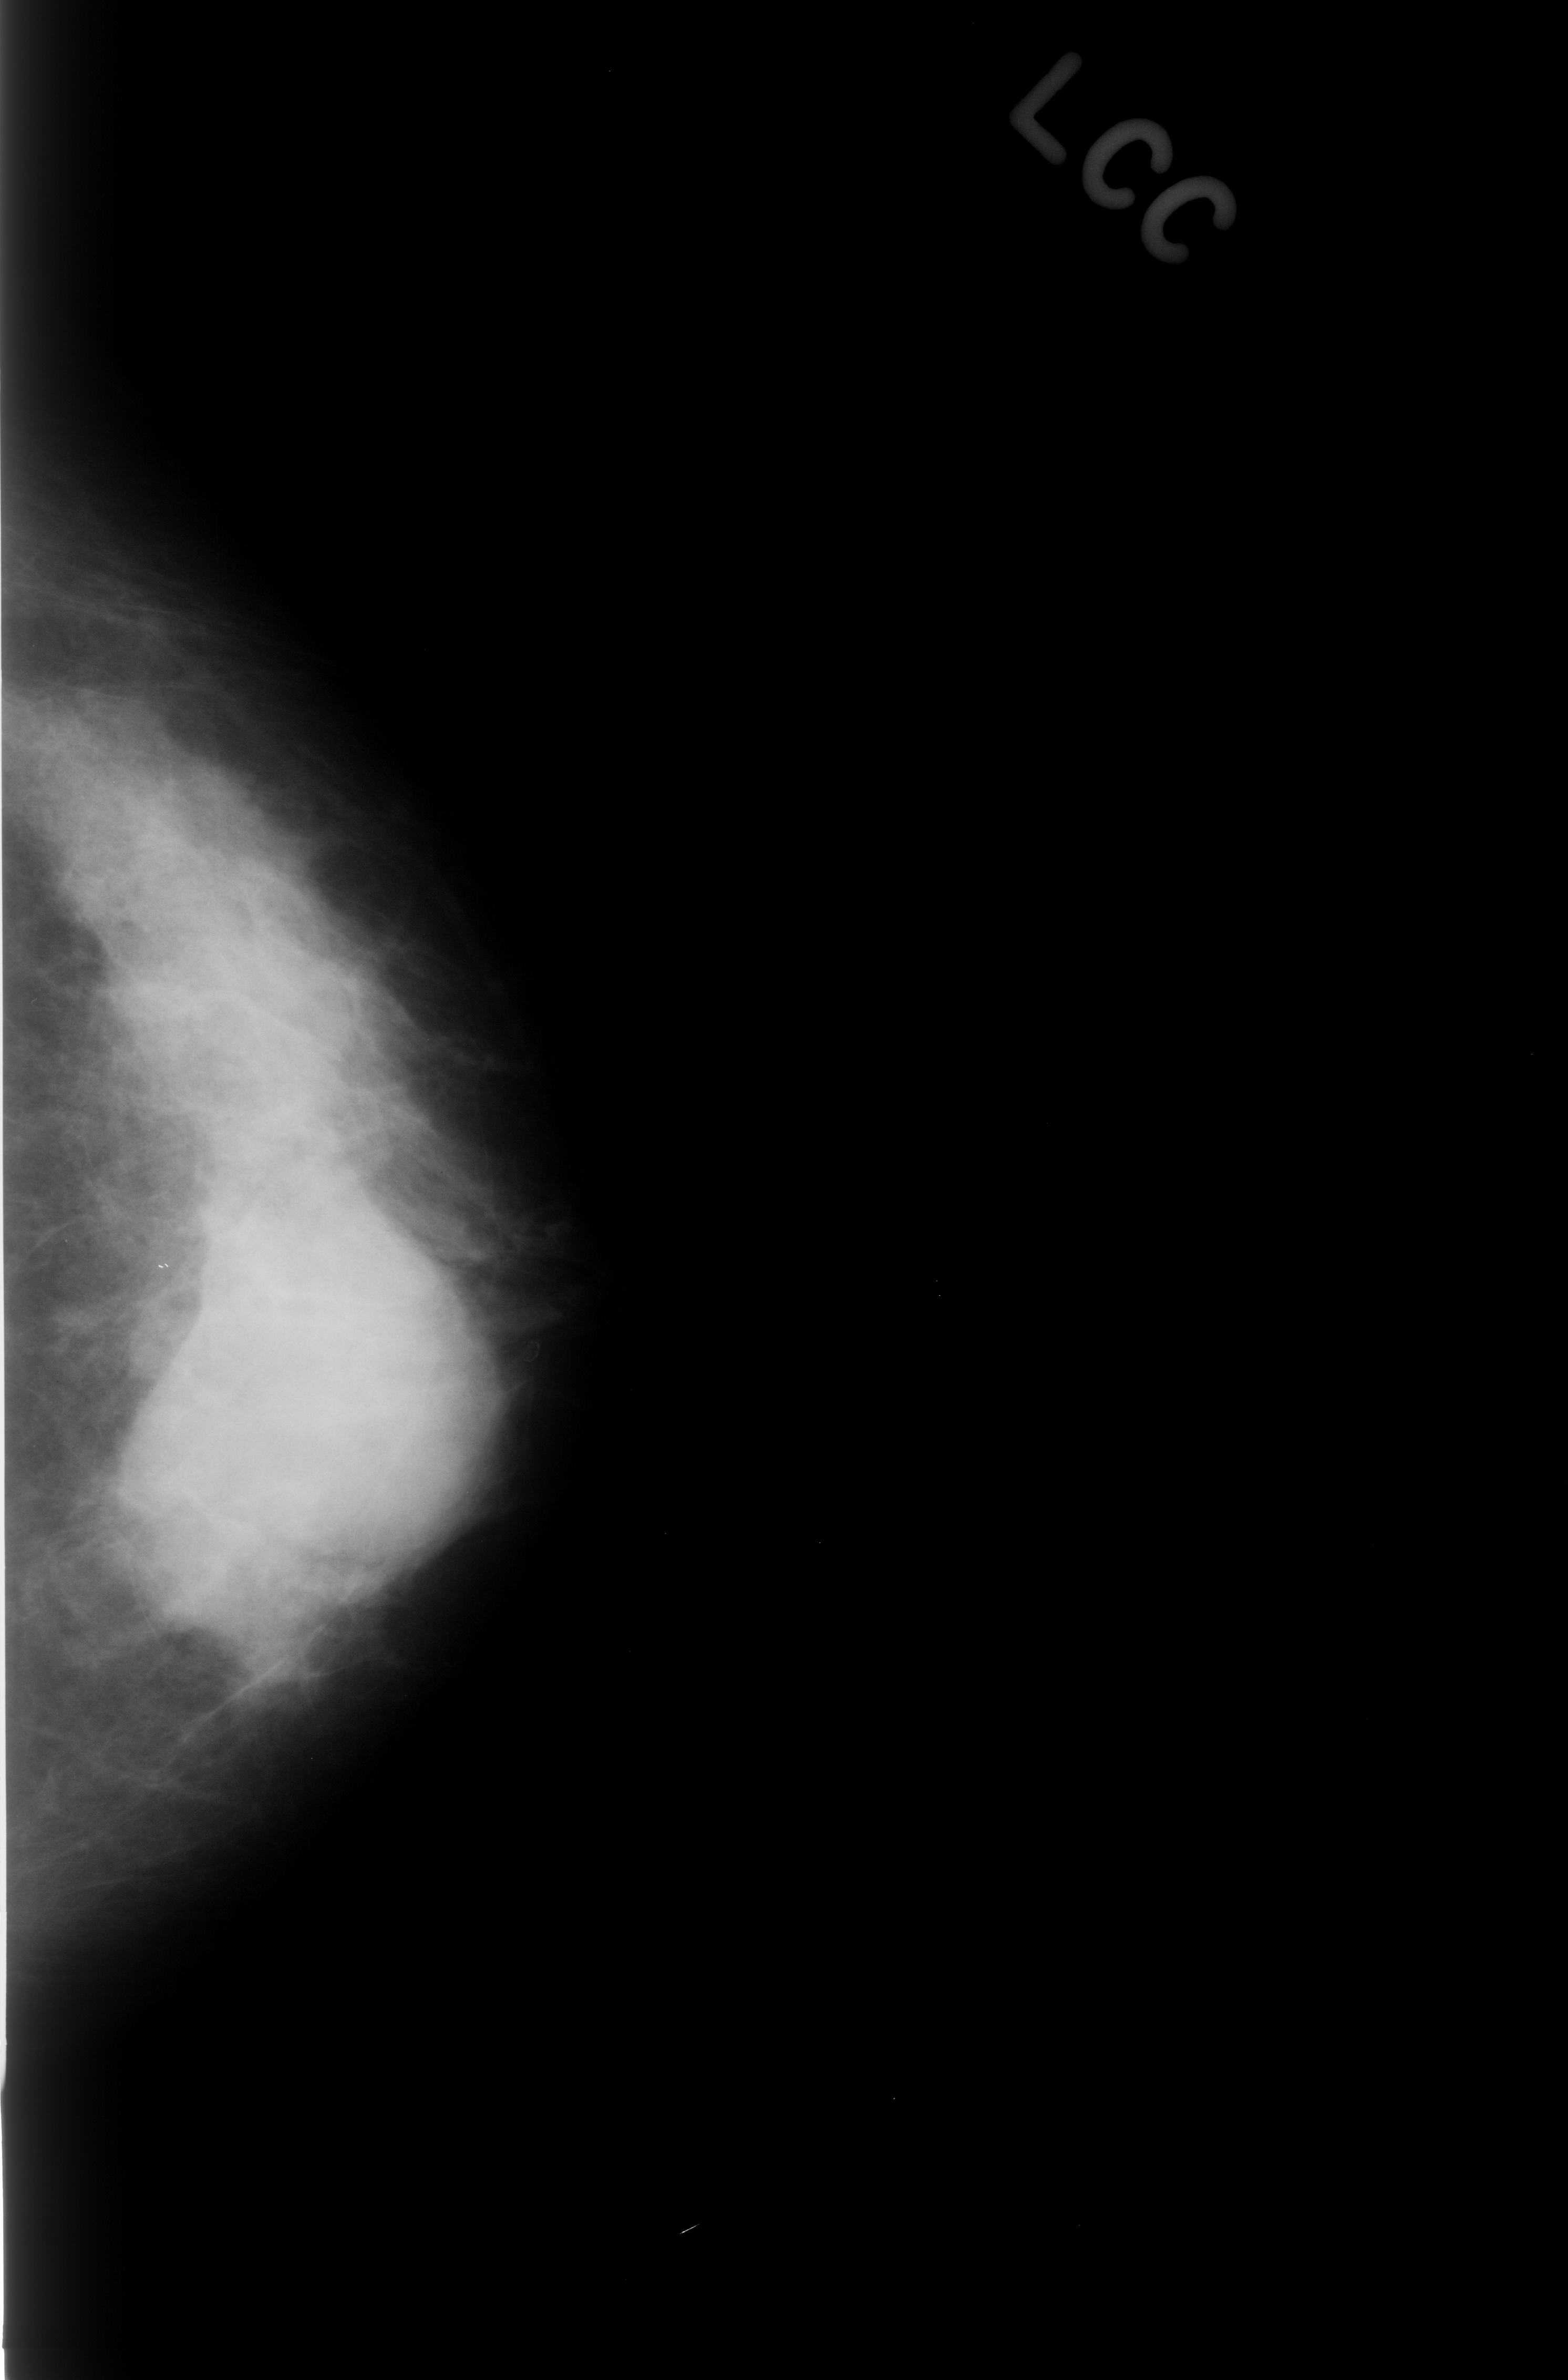
Mammogram (digitized film), left breast, craniocaudal (CC) view, BI-RADS breast density category 4 (scale 1–4).
Marked abnormality: mass, shape round, margins obscured; BI-RADS assessment category 4; pathology (as recorded): benign.